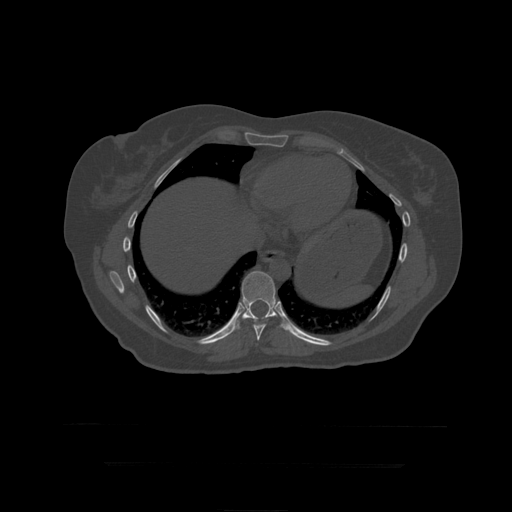
CT including the spine, one axial slice. Position 250 of 399 along the scan axis. Bone window (W 1800 / L 400 HU). 512 × 512 image matrix. Patient age 41 years. From the clinical record (not read from this slice): primary cancer: breast.
Annotated regions visible in this slice (semi-automatic segmentation, software-assisted and operator-edited):
- T10 vertebra: bounding box (x1, y1, x2, y2) in pixels: (233, 271, 279, 331)
- T9 vertebra: (253, 320, 268, 341)